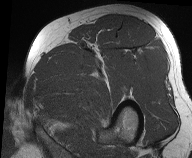
MRI of an extremity soft-tissue mass, one axial slice. Position 46 of 61 along the scan axis. MR volume resampled by the dataset authors to the PET/CT grid (not the native acquisition matrix). 3.27 mm slice thickness. 192 × 158 image matrix, field of view 187 × 154 mm. Male patient. Case-level facts recorded for this patient, not image findings: histological type: pleiomorphic liposarcoma; grade: high; site of the primary tumour: left thigh.
Structures marked on this image (expert contour drawn on MRI and transferred to this co-registered scan by the dataset authors):
- gross tumour volume including surrounding oedema: bounding box <32,98,60,120> (left, top, right, bottom; pixels)